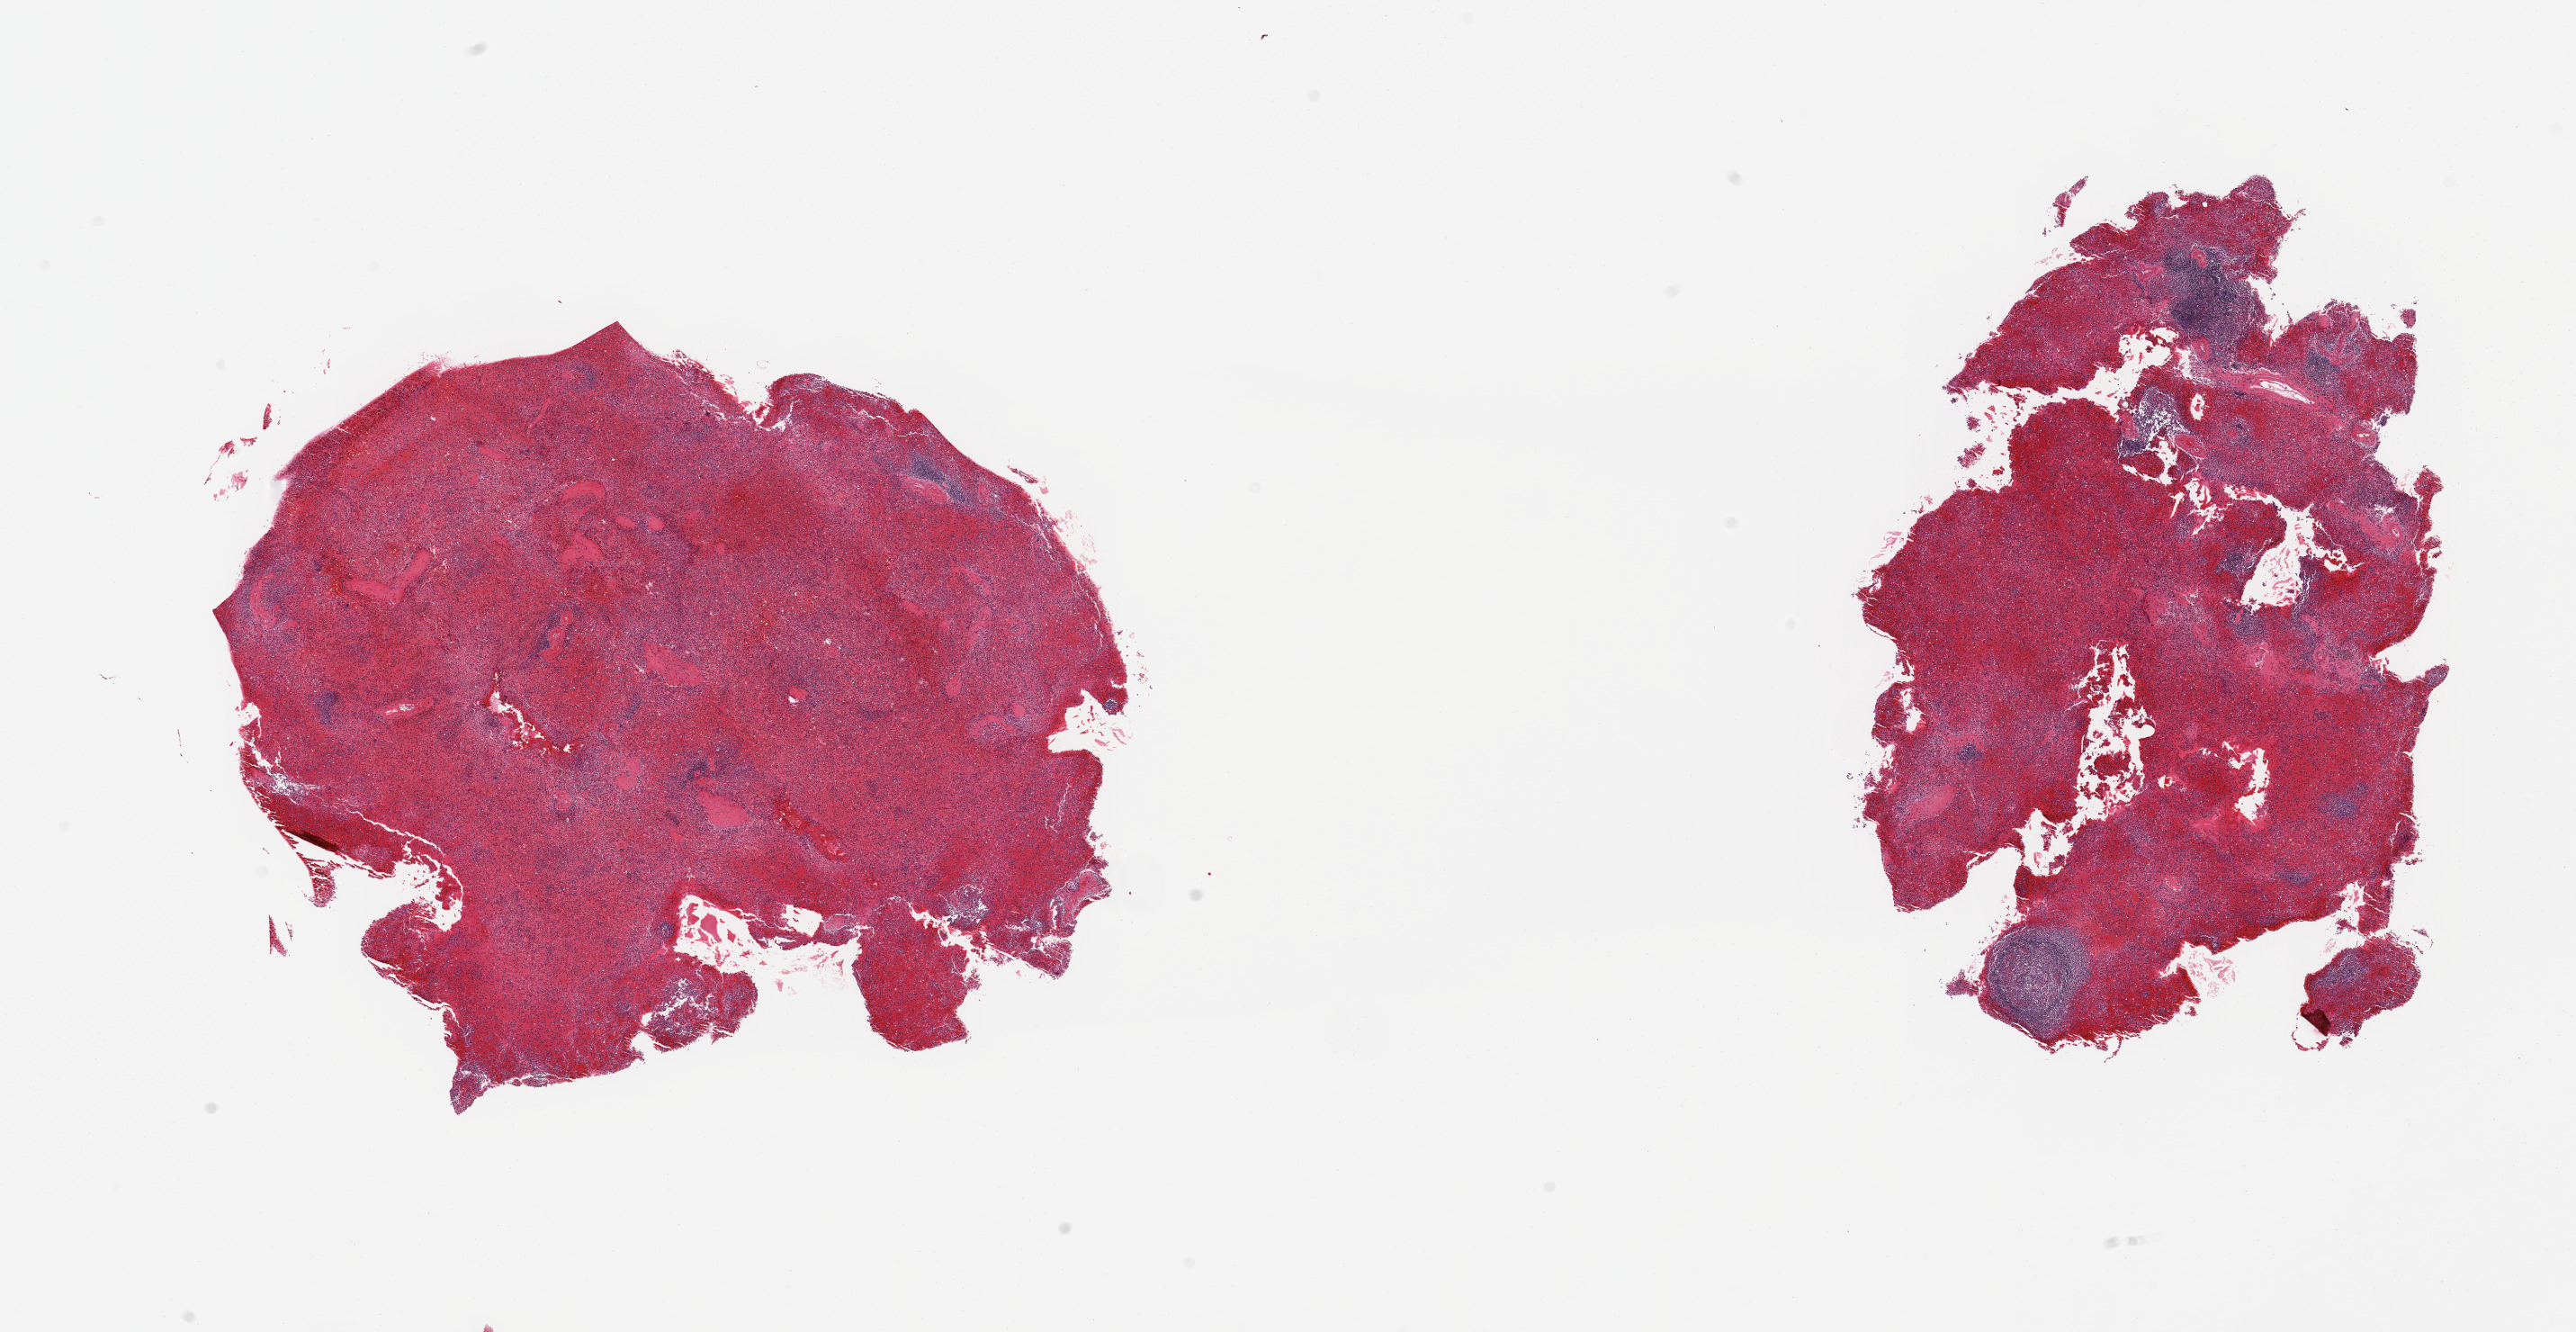
Whole-slide image, haematoxylin and eosin stain — whole scanned area (about 22.6 x 11.7 mm) shown as a low-resolution overview. PAXgene-fixed, paraffin-embedded tissue. Sampled site (target tissue): spleen. Tissue donor sample. Male donor.
Reviewer comment on this tissue sample: 2 pieces, marked congestion.